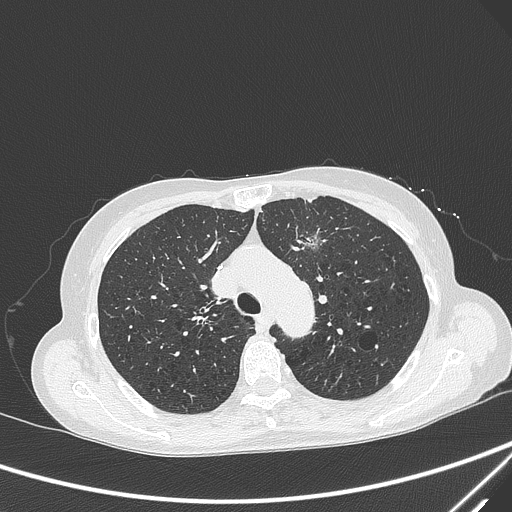
Chest CT, one axial slice. Slice 218 of 299 in the series (ordered by position). Lung window (W 1500 / L -600 HU). 1 mm slice thickness. 512 × 512 image matrix, field of view 350 × 350 mm. Patient: female, 71 years. Case-level facts recorded for this patient, not image findings: clinical TNM (as recorded): T1c N0 M0; histopathological grade: G2-3.
Structures marked on this image (bounding box drawn by a radiologist):
- lung tumour (recorded histology: adenocarcinoma): bounding box [x1, y1, x2, y2] px = [300, 227, 337, 262]